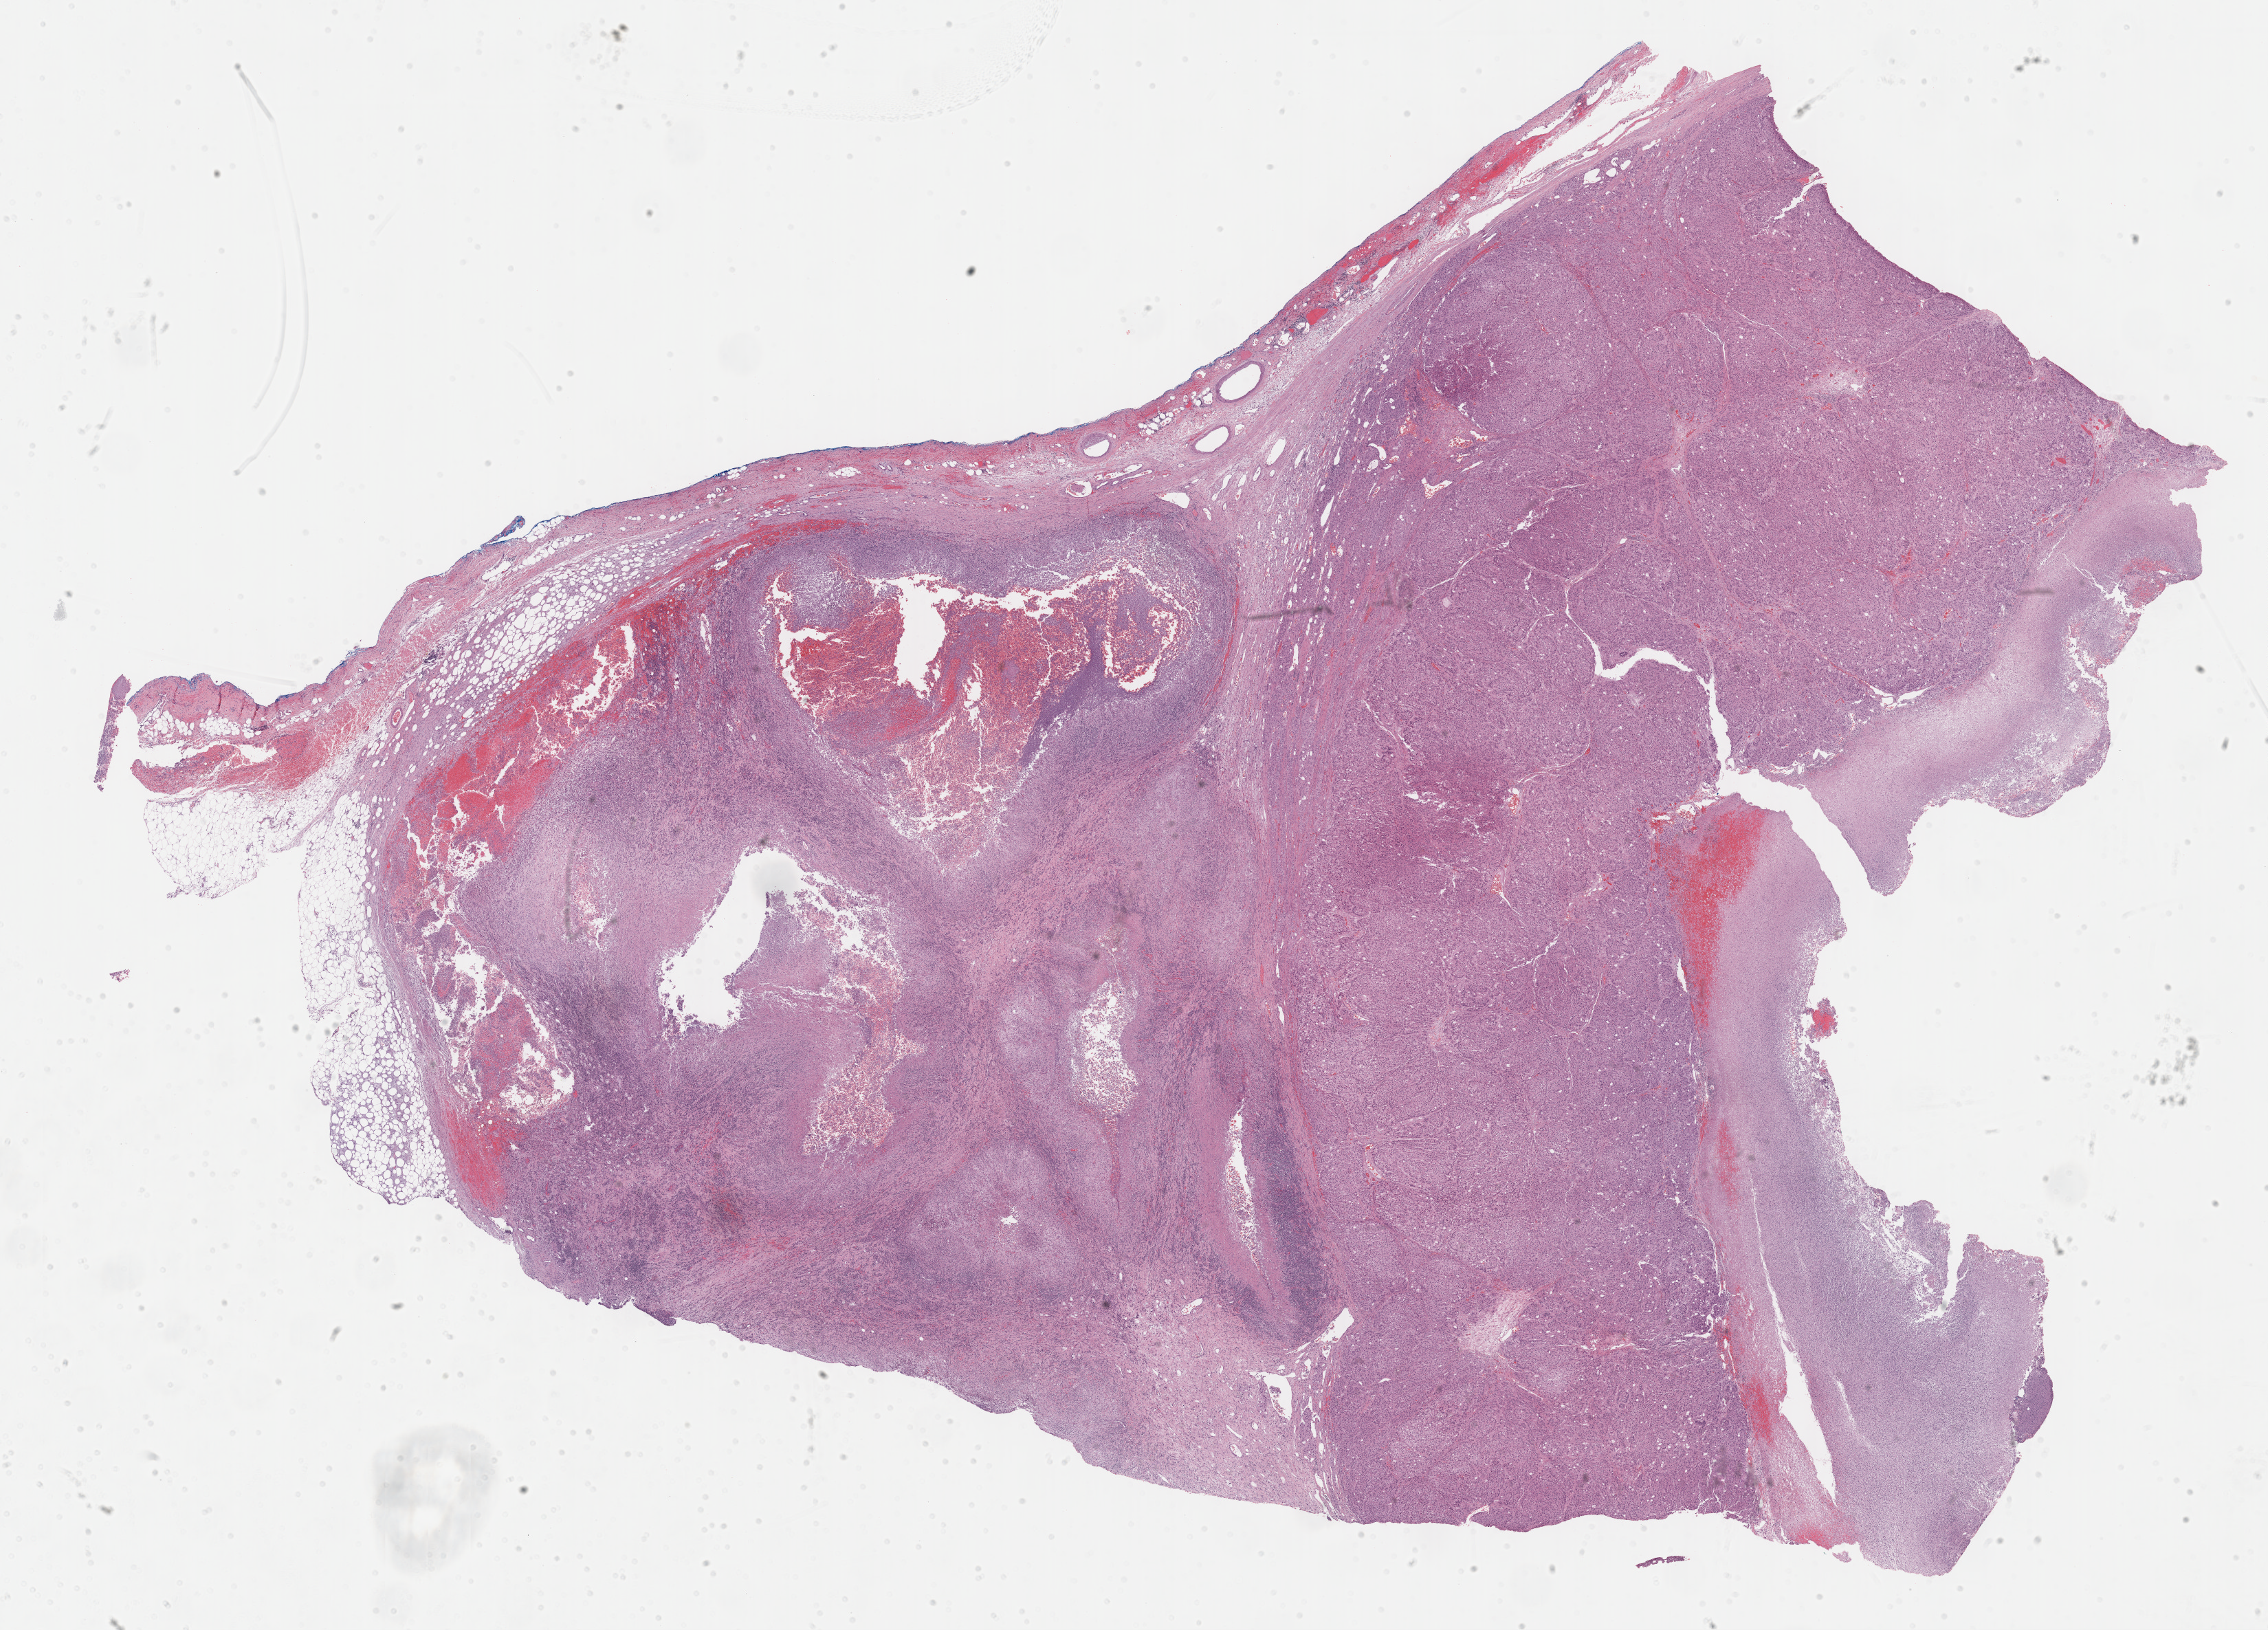
Hematoxylin and eosin (H&E) stained whole-slide image, low-resolution overview of the scanned area, about 26.7 x 19.2 mm (slide scanned at 40x), formalin-fixed paraffin-embedded (FFPE) diagnostic section, primary tumour sample from the adrenal cortex. Patient: female, age at initial diagnosis 65 years.
- pathologic diagnosis: Adrenal cortical carcinoma